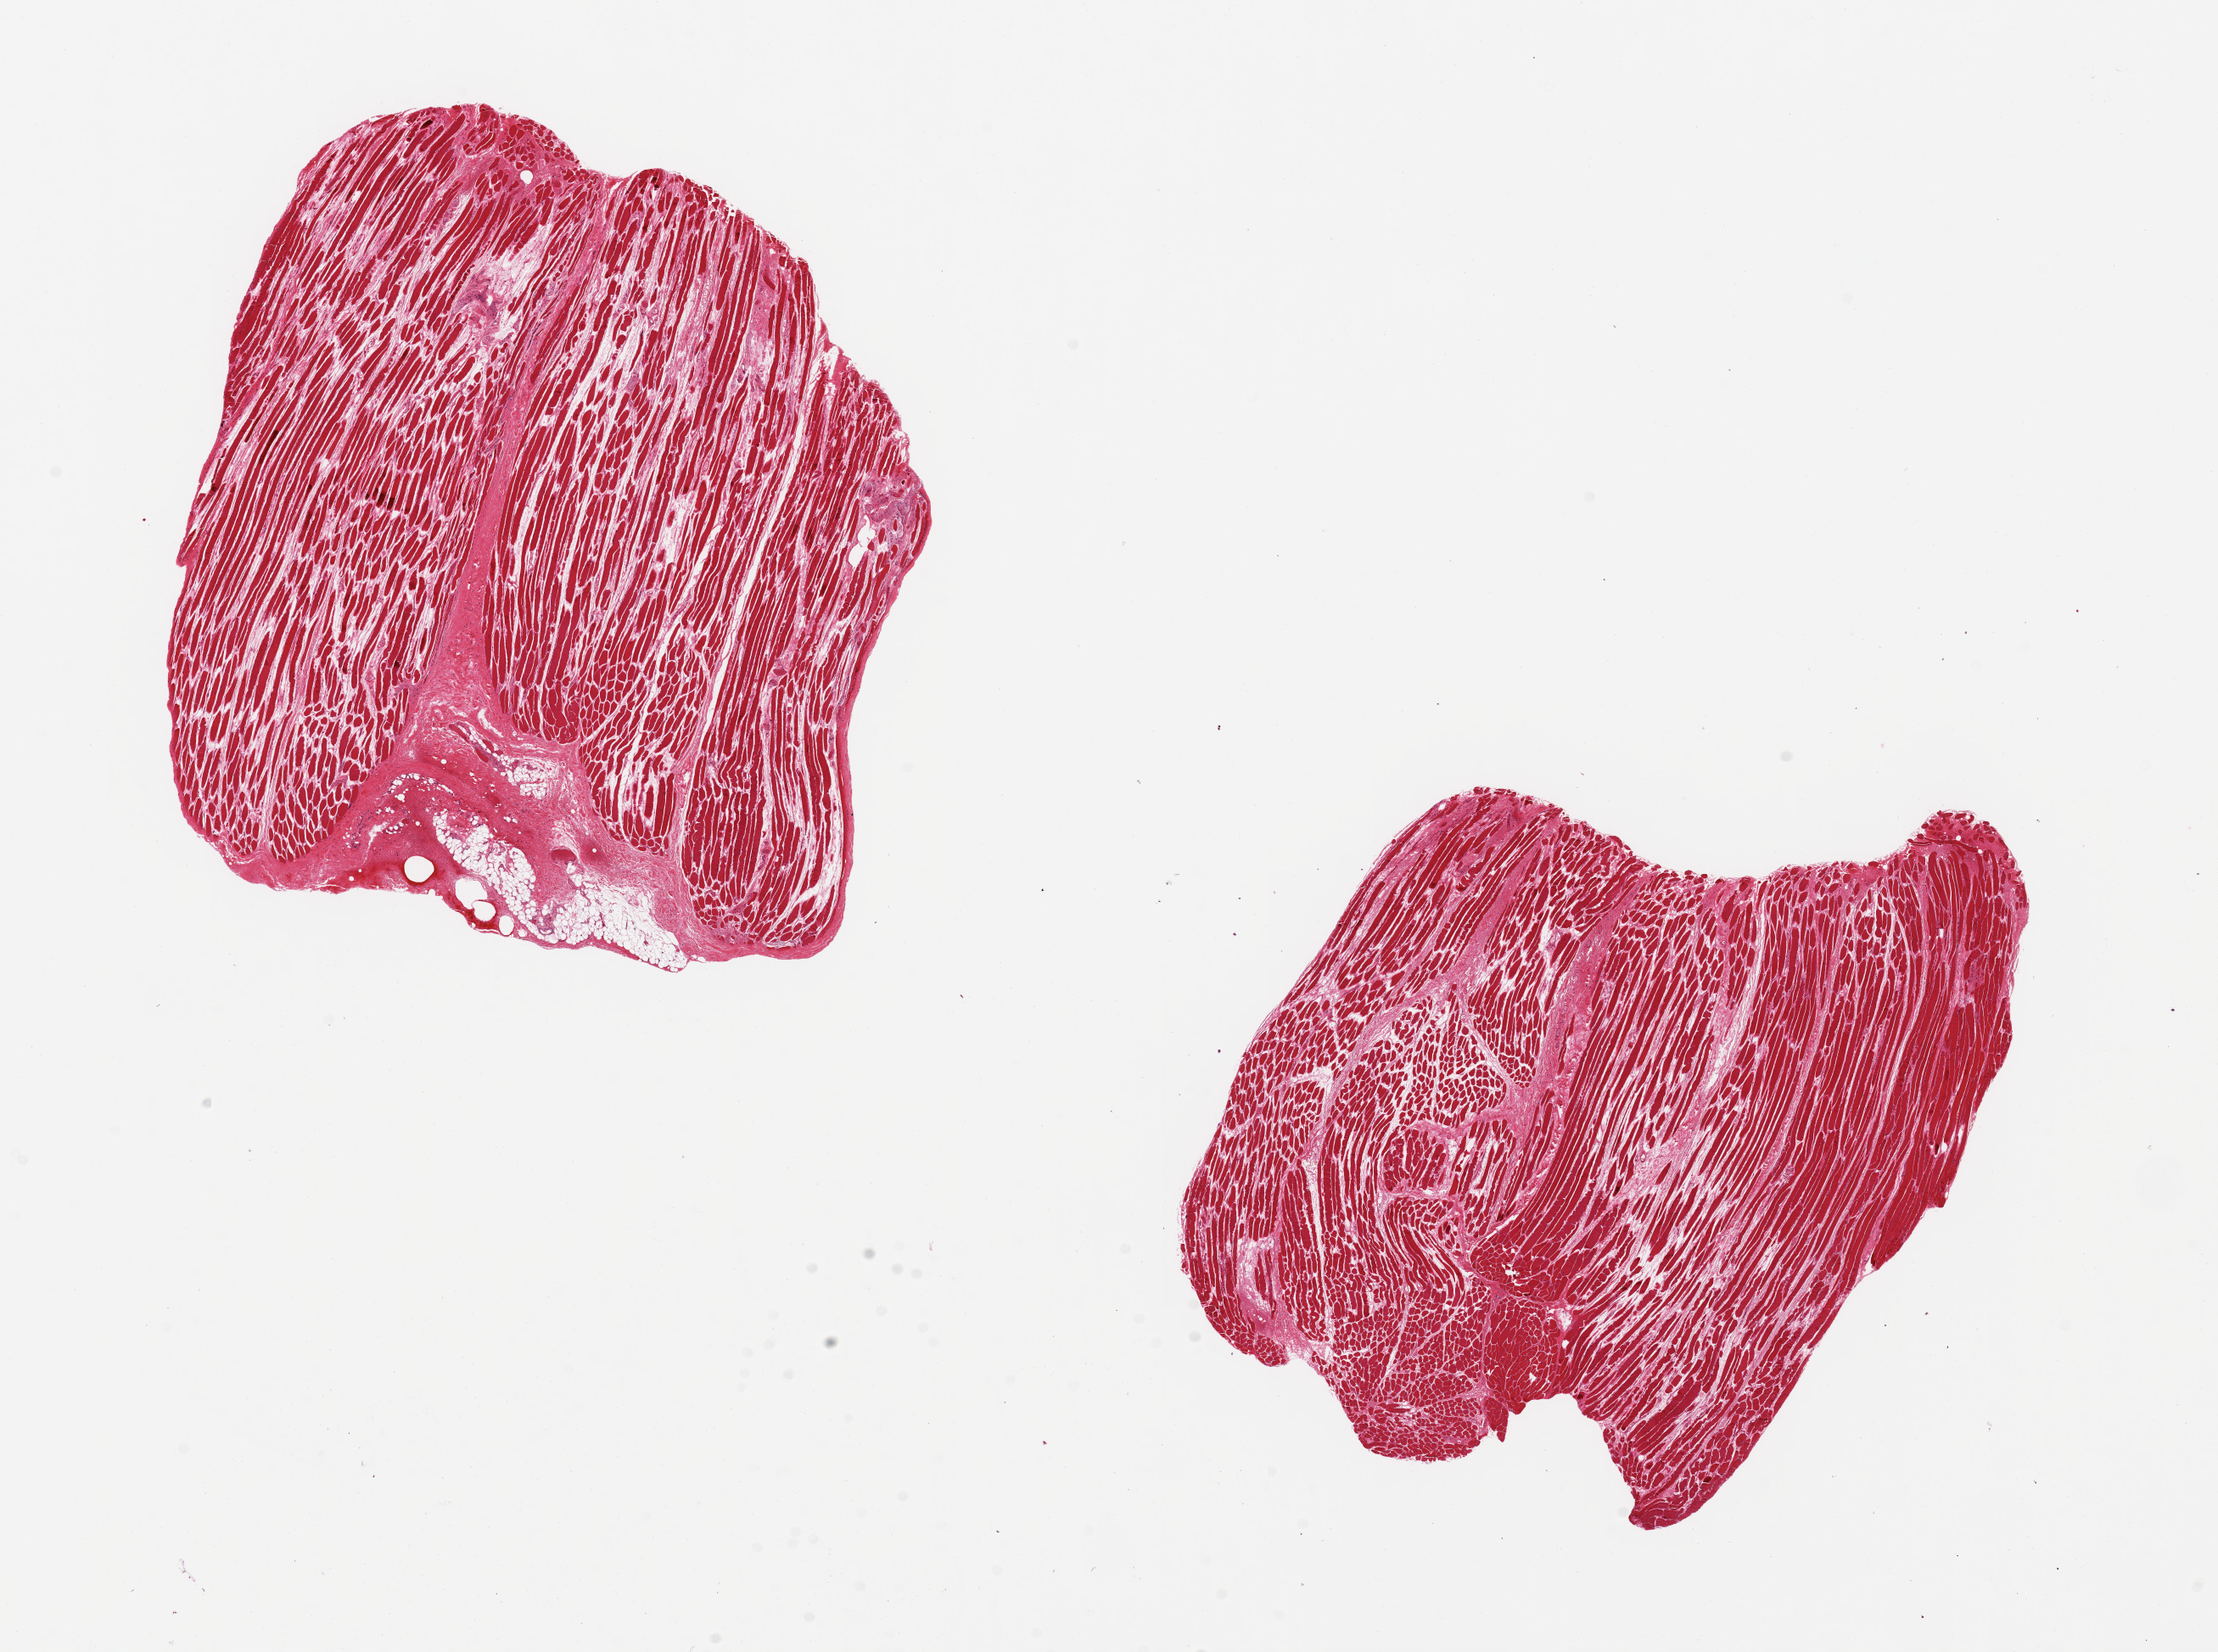
Haematoxylin and eosin whole-slide image, a low-resolution overview of the entire scanned area, about 20.7 x 15.4 mm (slide scanned at 20x). PAXgene-fixed, paraffin-embedded tissue. Section of thyroid (target tissue). Donor tissue sample. Male donor.
Review note (as recorded): 2 aliquots, ~6x6mm. INCORRECT TISSUE: SKELETAL MUSCLE, UNCERTAIN PROVENANCE.